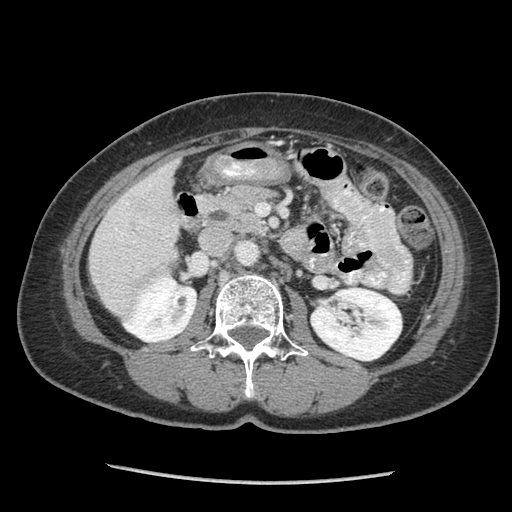
Contrast-enhanced abdominal CT (liver protocol), one axial slice; 140 kVp; soft-tissue window (W 400 / L 40 HU); 2.5 mm slice thickness; 512 × 512 image matrix, field of view 340 × 340 mm. From the clinical record (not read from this slice): diagnosis: hepatocellular carcinoma (patient treated with transarterial chemoembolisation; whether this scan precedes or follows treatment is not stated here); TNM stage (as recorded): Stage-I; Child-Pugh class: A; tumour nodularity: uninodular; tumour size: 11.1 cm.
Structures marked on this image (semi-automatically segmented with operator editing):
- liver parenchyma outside the tumour (the mass and vessels are separate outlines, so this box may not span the whole liver): bounding box [x1, y1, x2, y2] px = [90, 158, 182, 314]
- liver vessels: [103, 184, 152, 264]